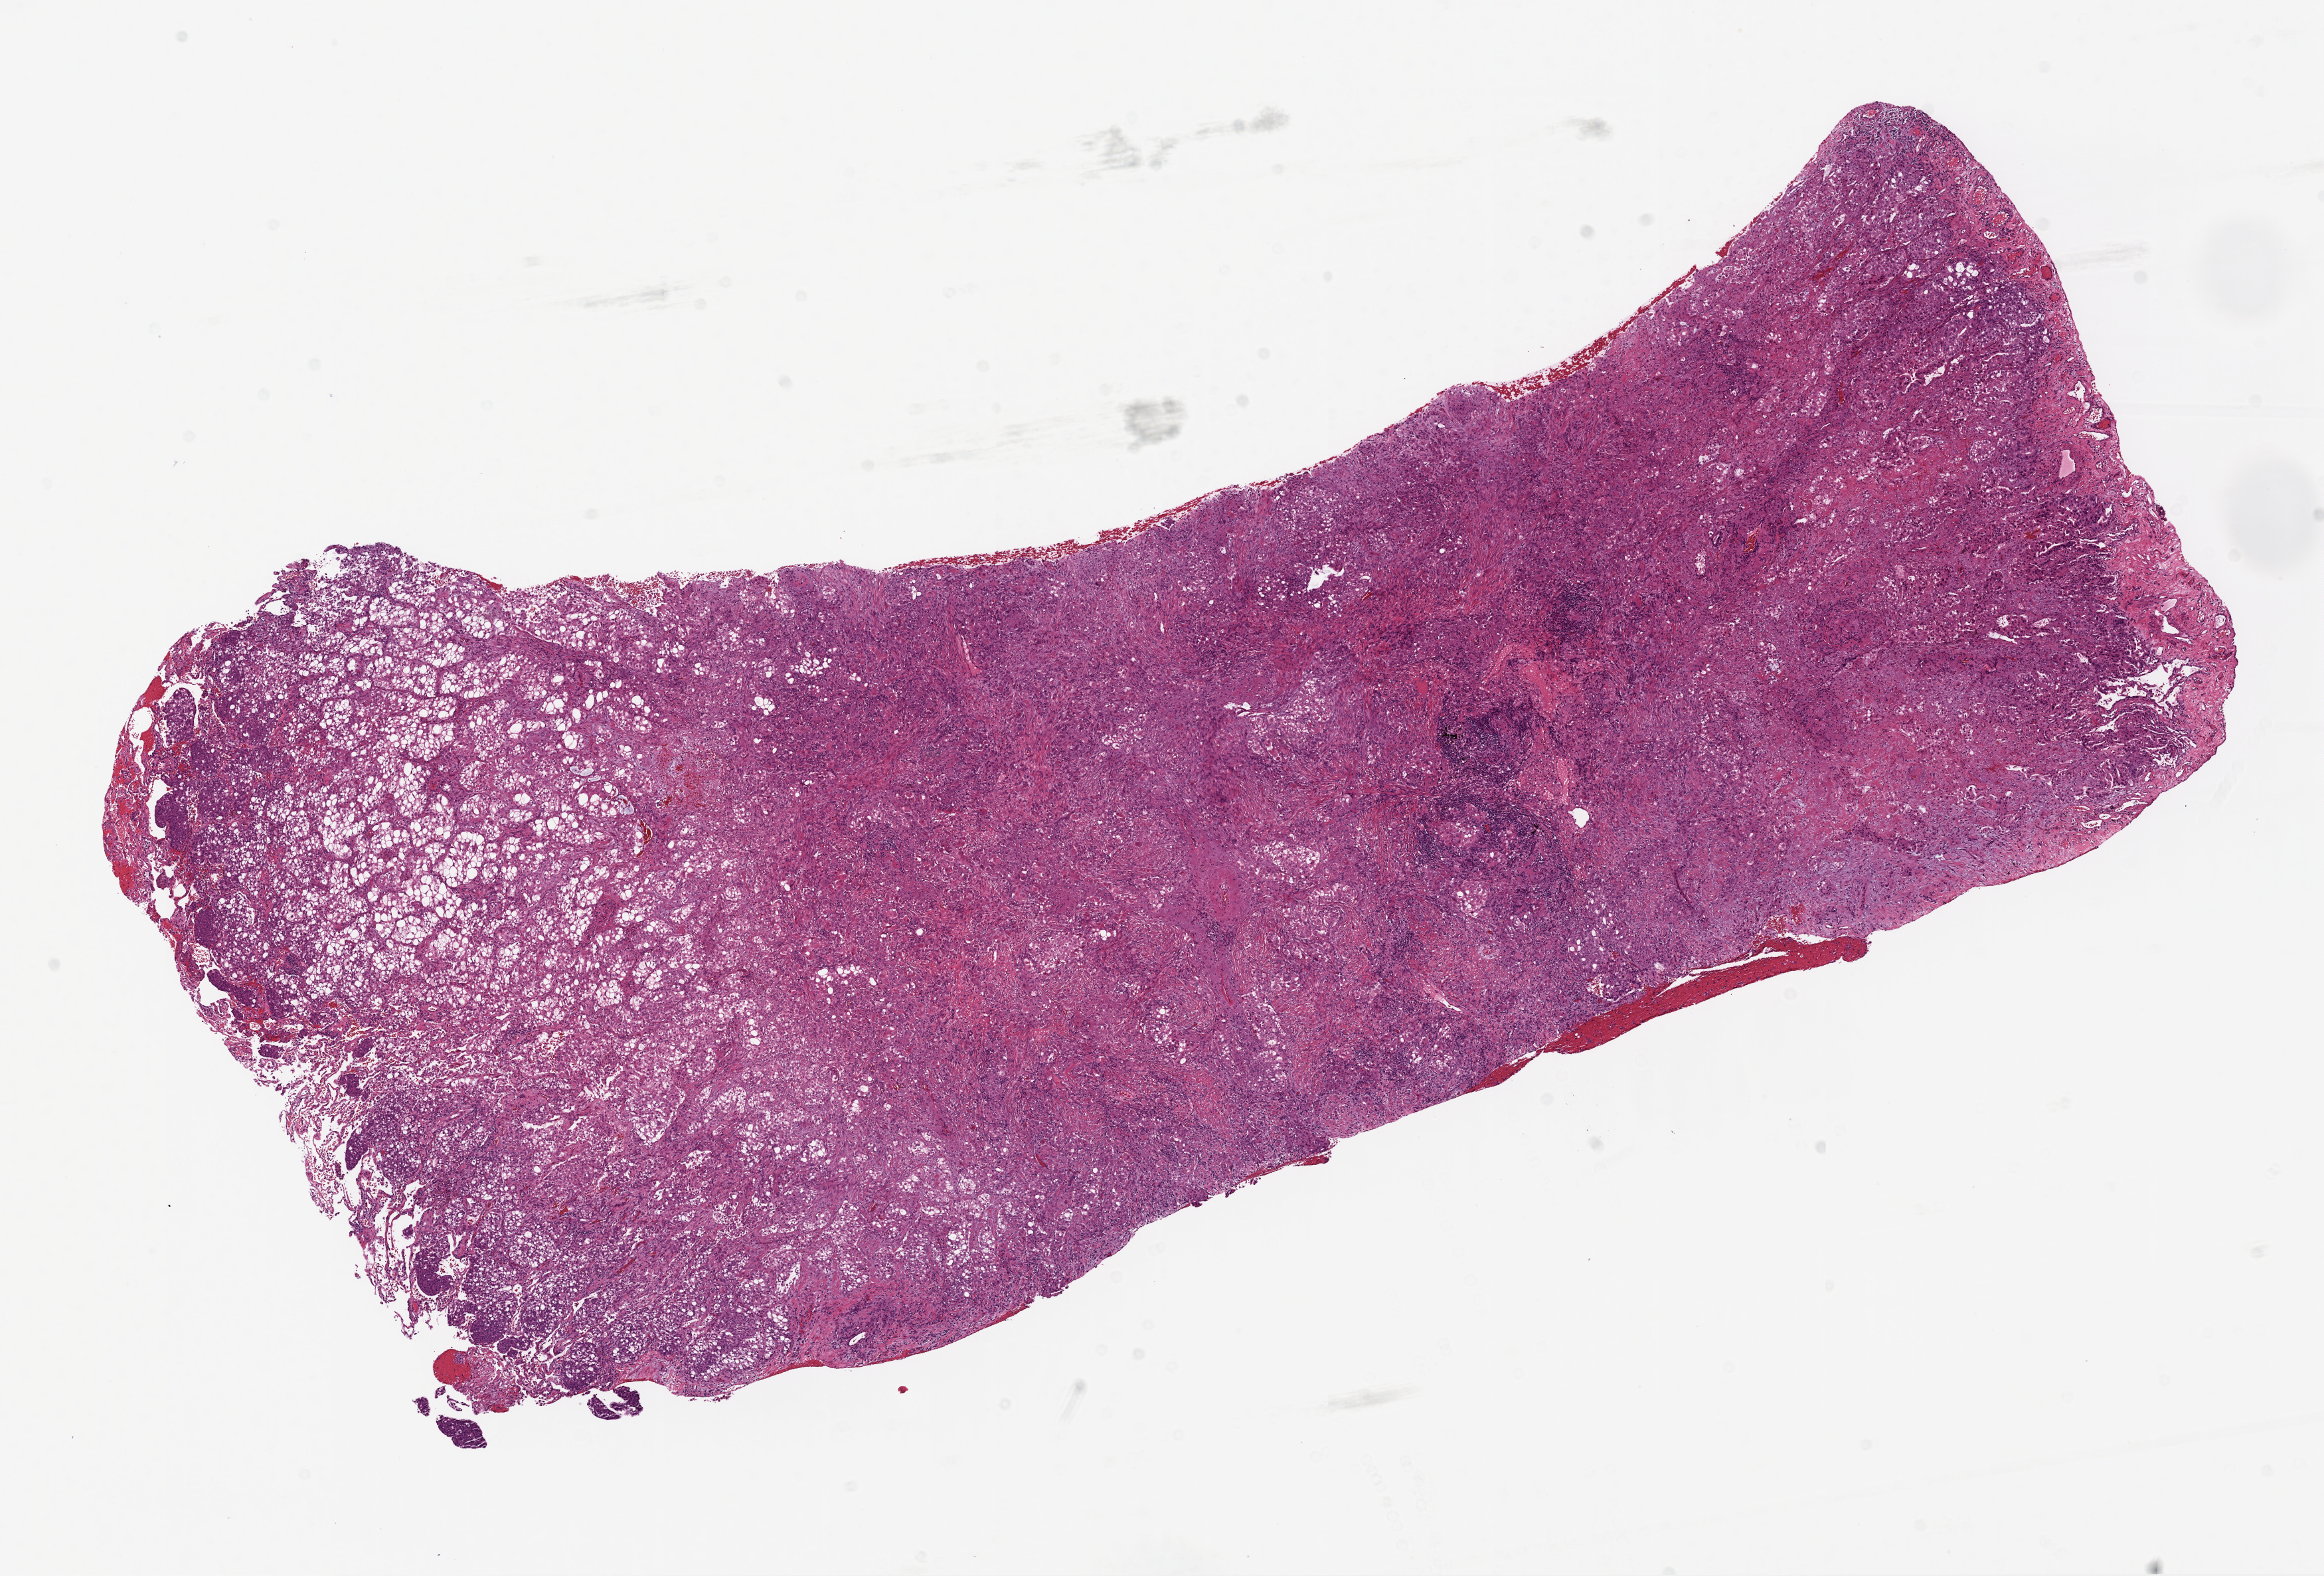
Digitized Hematoxylin and eosin (H&E) stained tissue section (whole slide), low-resolution overview of the scanned area, about 14.0 x 9.5 mm, frozen section from the top of the tissue portion, primary tumour sample from the lung. Patient: female, age at initial diagnosis 77 years. Pathologist review of this section (percent, as recorded): tumour cells 70%, tumour nuclei 70%, normal cells 0%, stromal cells 30%, necrosis 0%.
TNM: T1b N0 M0. Histologic diagnosis: Adenocarcinoma, NOS (lower lobe, lung). Laterality: right. AJCC pathologic stage: IA (6th edition).